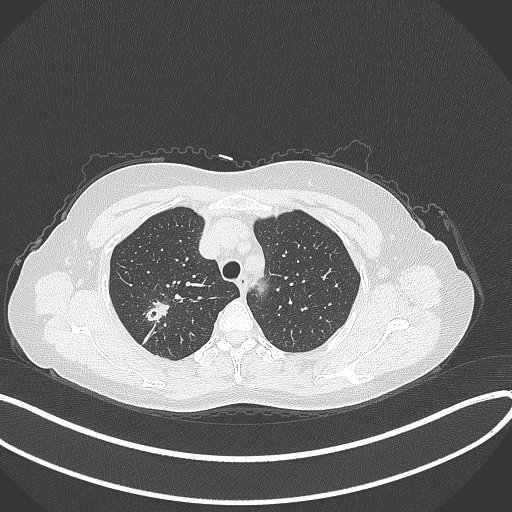
Chest CT, one axial slice; position 288 of 337 along the scan axis; lung window (W 1500 / L -600 HU); 1 mm slice thickness; 512 × 512 image matrix, field of view 400 × 400 mm. Female patient, age 50 years. Case-level facts recorded for this patient, not image findings: clinical TNM (as recorded): T1c N0 M0; histopathological grade: G2-3.
Outlined on this slice (rectangle marked by the reading radiologist):
- lung tumour (recorded histology: adenocarcinoma): bounding box (x1, y1, x2, y2) in pixels: (141, 297, 178, 330)